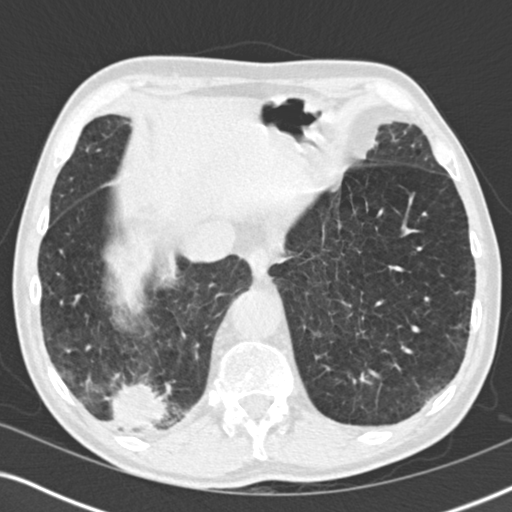
Chest CT (low-dose screening protocol), one axial image; baseline annual screen; lung window (W 1500 / L -600 HU); 2 mm slice thickness. Male, age 64 years at enrolment. Former smoker at enrolment.
Expert-annotated lung lesion, bounding box <77,364,179,451> (left, top, right, bottom; pixels). The screening reader recorded 3 non-calcified nodules or masses ≥4 mm on this exam; which of them this box marks is not recorded. Official screen result: positive, change unspecified: nodule(s) >= 4 mm or enlarging nodule(s), mass(es), or other non-specific abnormalities suspicious for lung cancer. Participant outcome: lung cancer diagnosed 27 days after this screen — squamous cell carcinoma, NOS, right lower lobe, moderately differentiated (G2), stage IV (AJCC 6th edition), 40 mm at pathology.